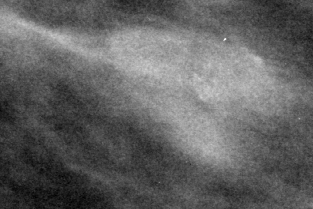
Cropped region of a digitized screen-film mammogram centred on a radiologist-marked abnormality, left breast, MLO view.
Finding: calcifications, morphology amorphous, distribution clustered; BI-RADS assessment category 4; pathology (as recorded): benign.